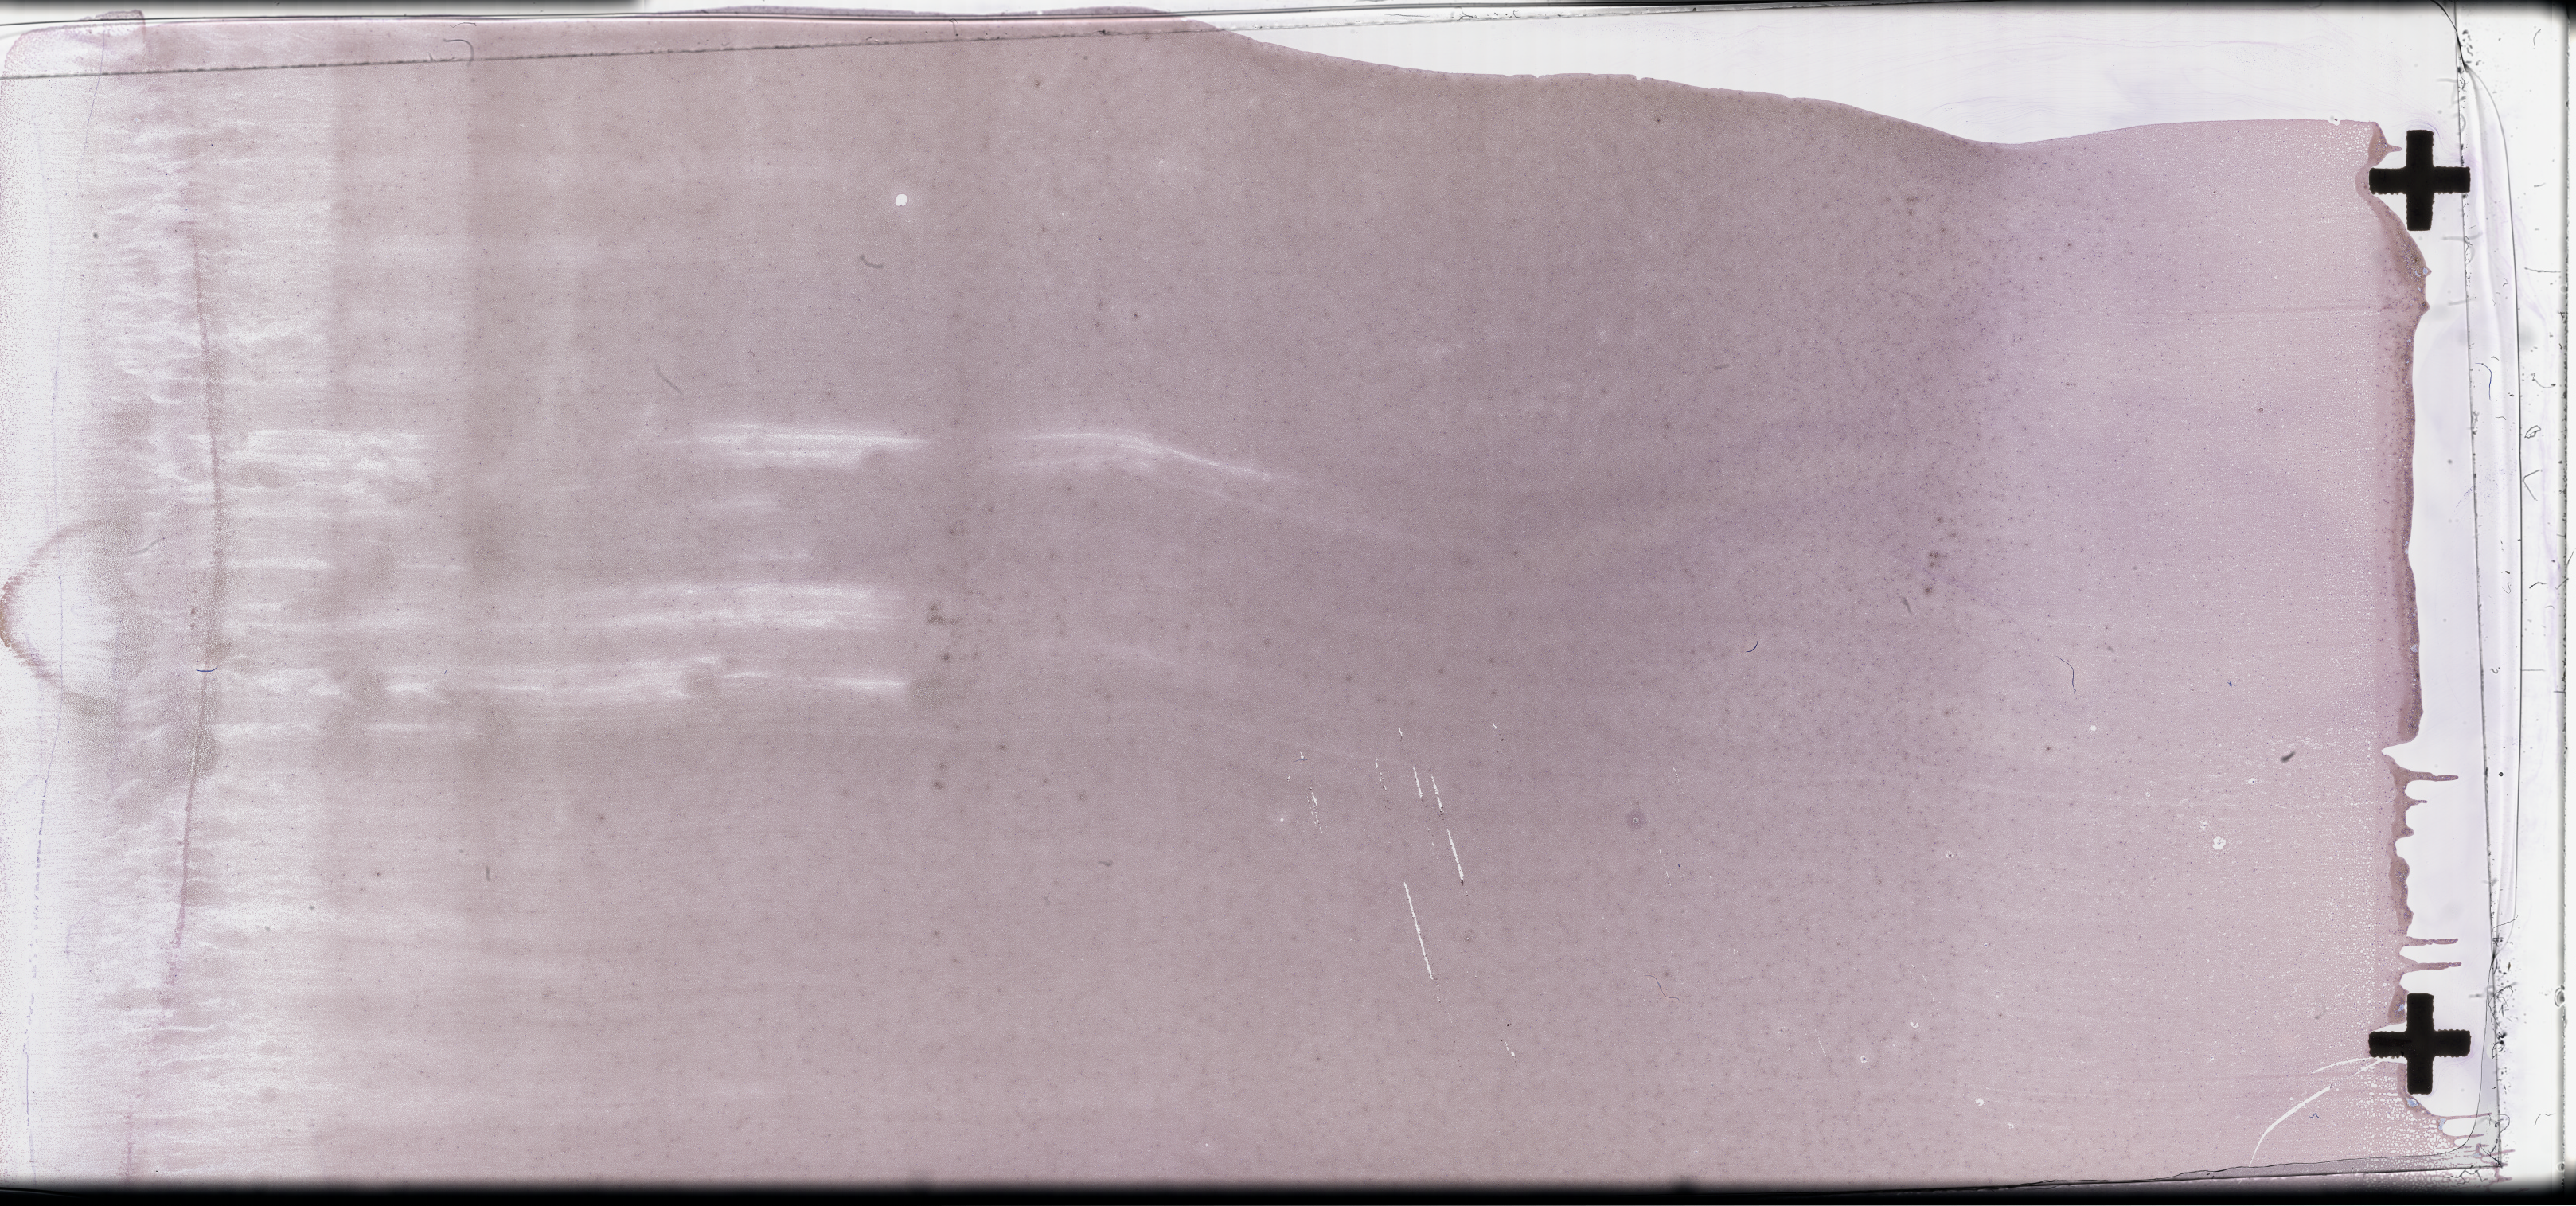
Wright–Giemsa-stained whole blood smear, whole-slide image — whole scanned area (about 52.3 x 24.5 mm) shown as a low-resolution overview, EDTA-anticoagulated smear, collected on treatment. Patient sex: male.
* from a patient with: Acute Myeloid Leukemia Not Otherwise Specified